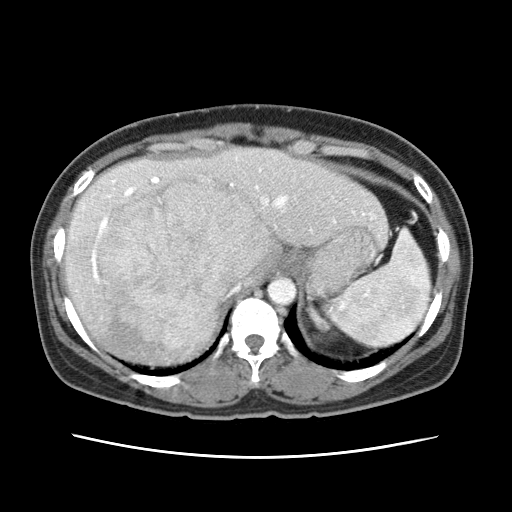
Contrast-enhanced abdominal CT (liver protocol), one axial slice; position 49 of 79 along the scan axis; 120 kVp; soft-tissue window (W 400 / L 40 HU); 2.5 mm slice thickness; 512 × 512 image matrix, field of view 340 × 340 mm. From the clinical record (not read from this slice): diagnosis: hepatocellular carcinoma (patient treated with transarterial chemoembolisation; whether this scan precedes or follows treatment is not stated here); TNM stage (as recorded): Stage-I; Child-Pugh class: A.
Outlined on this slice (semi-automatically segmented with operator editing):
- abdominal aorta: bounding box [x1, y1, x2, y2] px = [267, 278, 296, 304]
- liver parenchyma outside the tumour (the mass and vessels are separate outlines, so this box may not span the whole liver): [64, 148, 384, 364]
- mass: [98, 178, 270, 346]
- liver vessels: [83, 169, 372, 281]